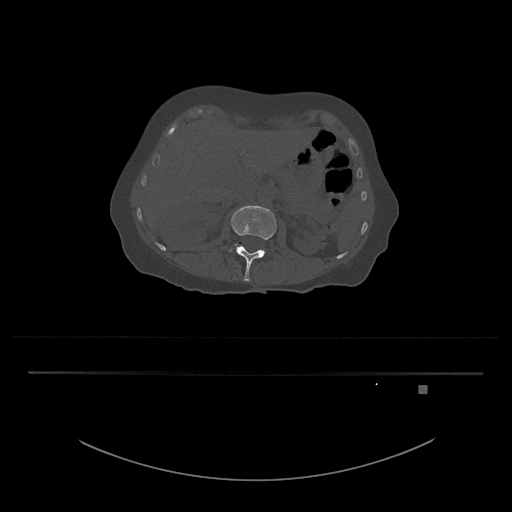
CT including the spine, one axial slice. Slice 483 of 797 in the series (ordered by position). Reconstruction kernel Br40s/3. 120 kVp. Bone window (W 1800 / L 400 HU). 512 × 512 image matrix, field of view 500 × 500 mm. Female patient, age 57 years. Case-level facts recorded for this patient, not image findings: primary cancer: cervical.
Annotated regions visible in this slice (semi-automatic segmentation, software-assisted and operator-edited):
- L3 vertebra: bounding box (x1, y1, x2, y2) in pixels: (230, 244, 237, 252)